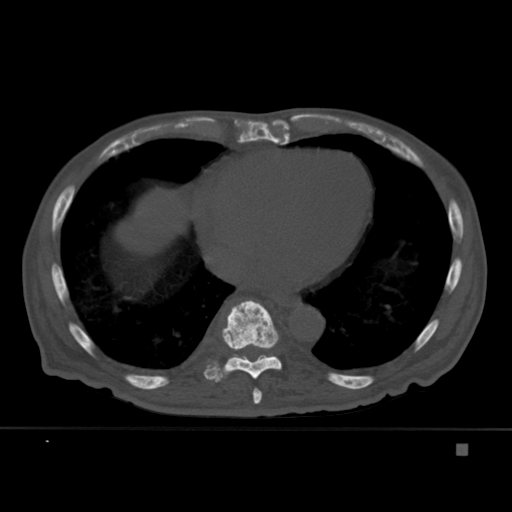
CT including the spine, one axial slice; bone window (W 1800 / L 400 HU); 1.5 mm slice thickness; 512 × 512 image matrix, field of view 378 × 378 mm. Male patient, age 75 years. Case-level facts recorded for this patient, not image findings: primary cancer: prostate.
Structures marked on this image (semi-automatic segmentation, software-assisted and operator-edited):
- T10 vertebra: bounding box <232,354,271,359> (left, top, right, bottom; pixels)
- T8 vertebra: <251,375,262,404>
- T9 vertebra: <203,300,282,383>